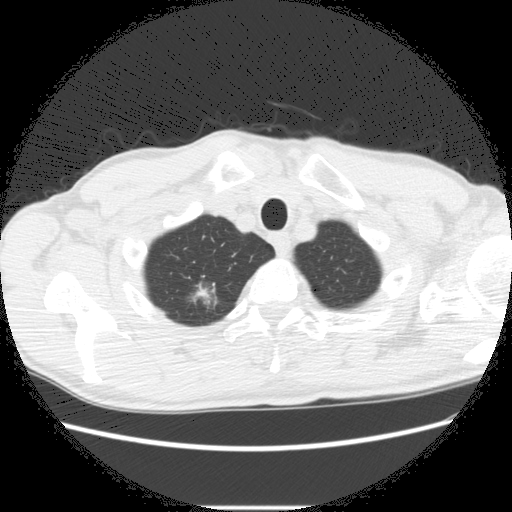
Chest CT (low-dose screening protocol), one axial image; second screening round (one year after baseline); lung window (W 1500 / L -600 HU); 2.5 mm slice thickness; slice 25 of 282 in the series. Male, age 66 years at enrolment. Former smoker at enrolment.
Lesion marked by an expert reader, bounding box (x1, y1, x2, y2) in pixels: (172, 277, 233, 326). The screening reader recorded 5 non-calcified nodules or masses ≥4 mm on this exam (right lower lobe, right upper lobe, right upper lobe, right upper lobe, left lower lobe); which of them this box marks is not recorded. Official screen result: positive, change unspecified: nodule(s) >= 4 mm or enlarging nodule(s), mass(es), or other non-specific abnormalities suspicious for lung cancer. Later outcome: lung cancer diagnosed 75 days after this screen — adenocarcinoma, NOS, right upper lobe, undifferentiated (G4), stage IA (AJCC 6th edition), 20 mm at pathology.